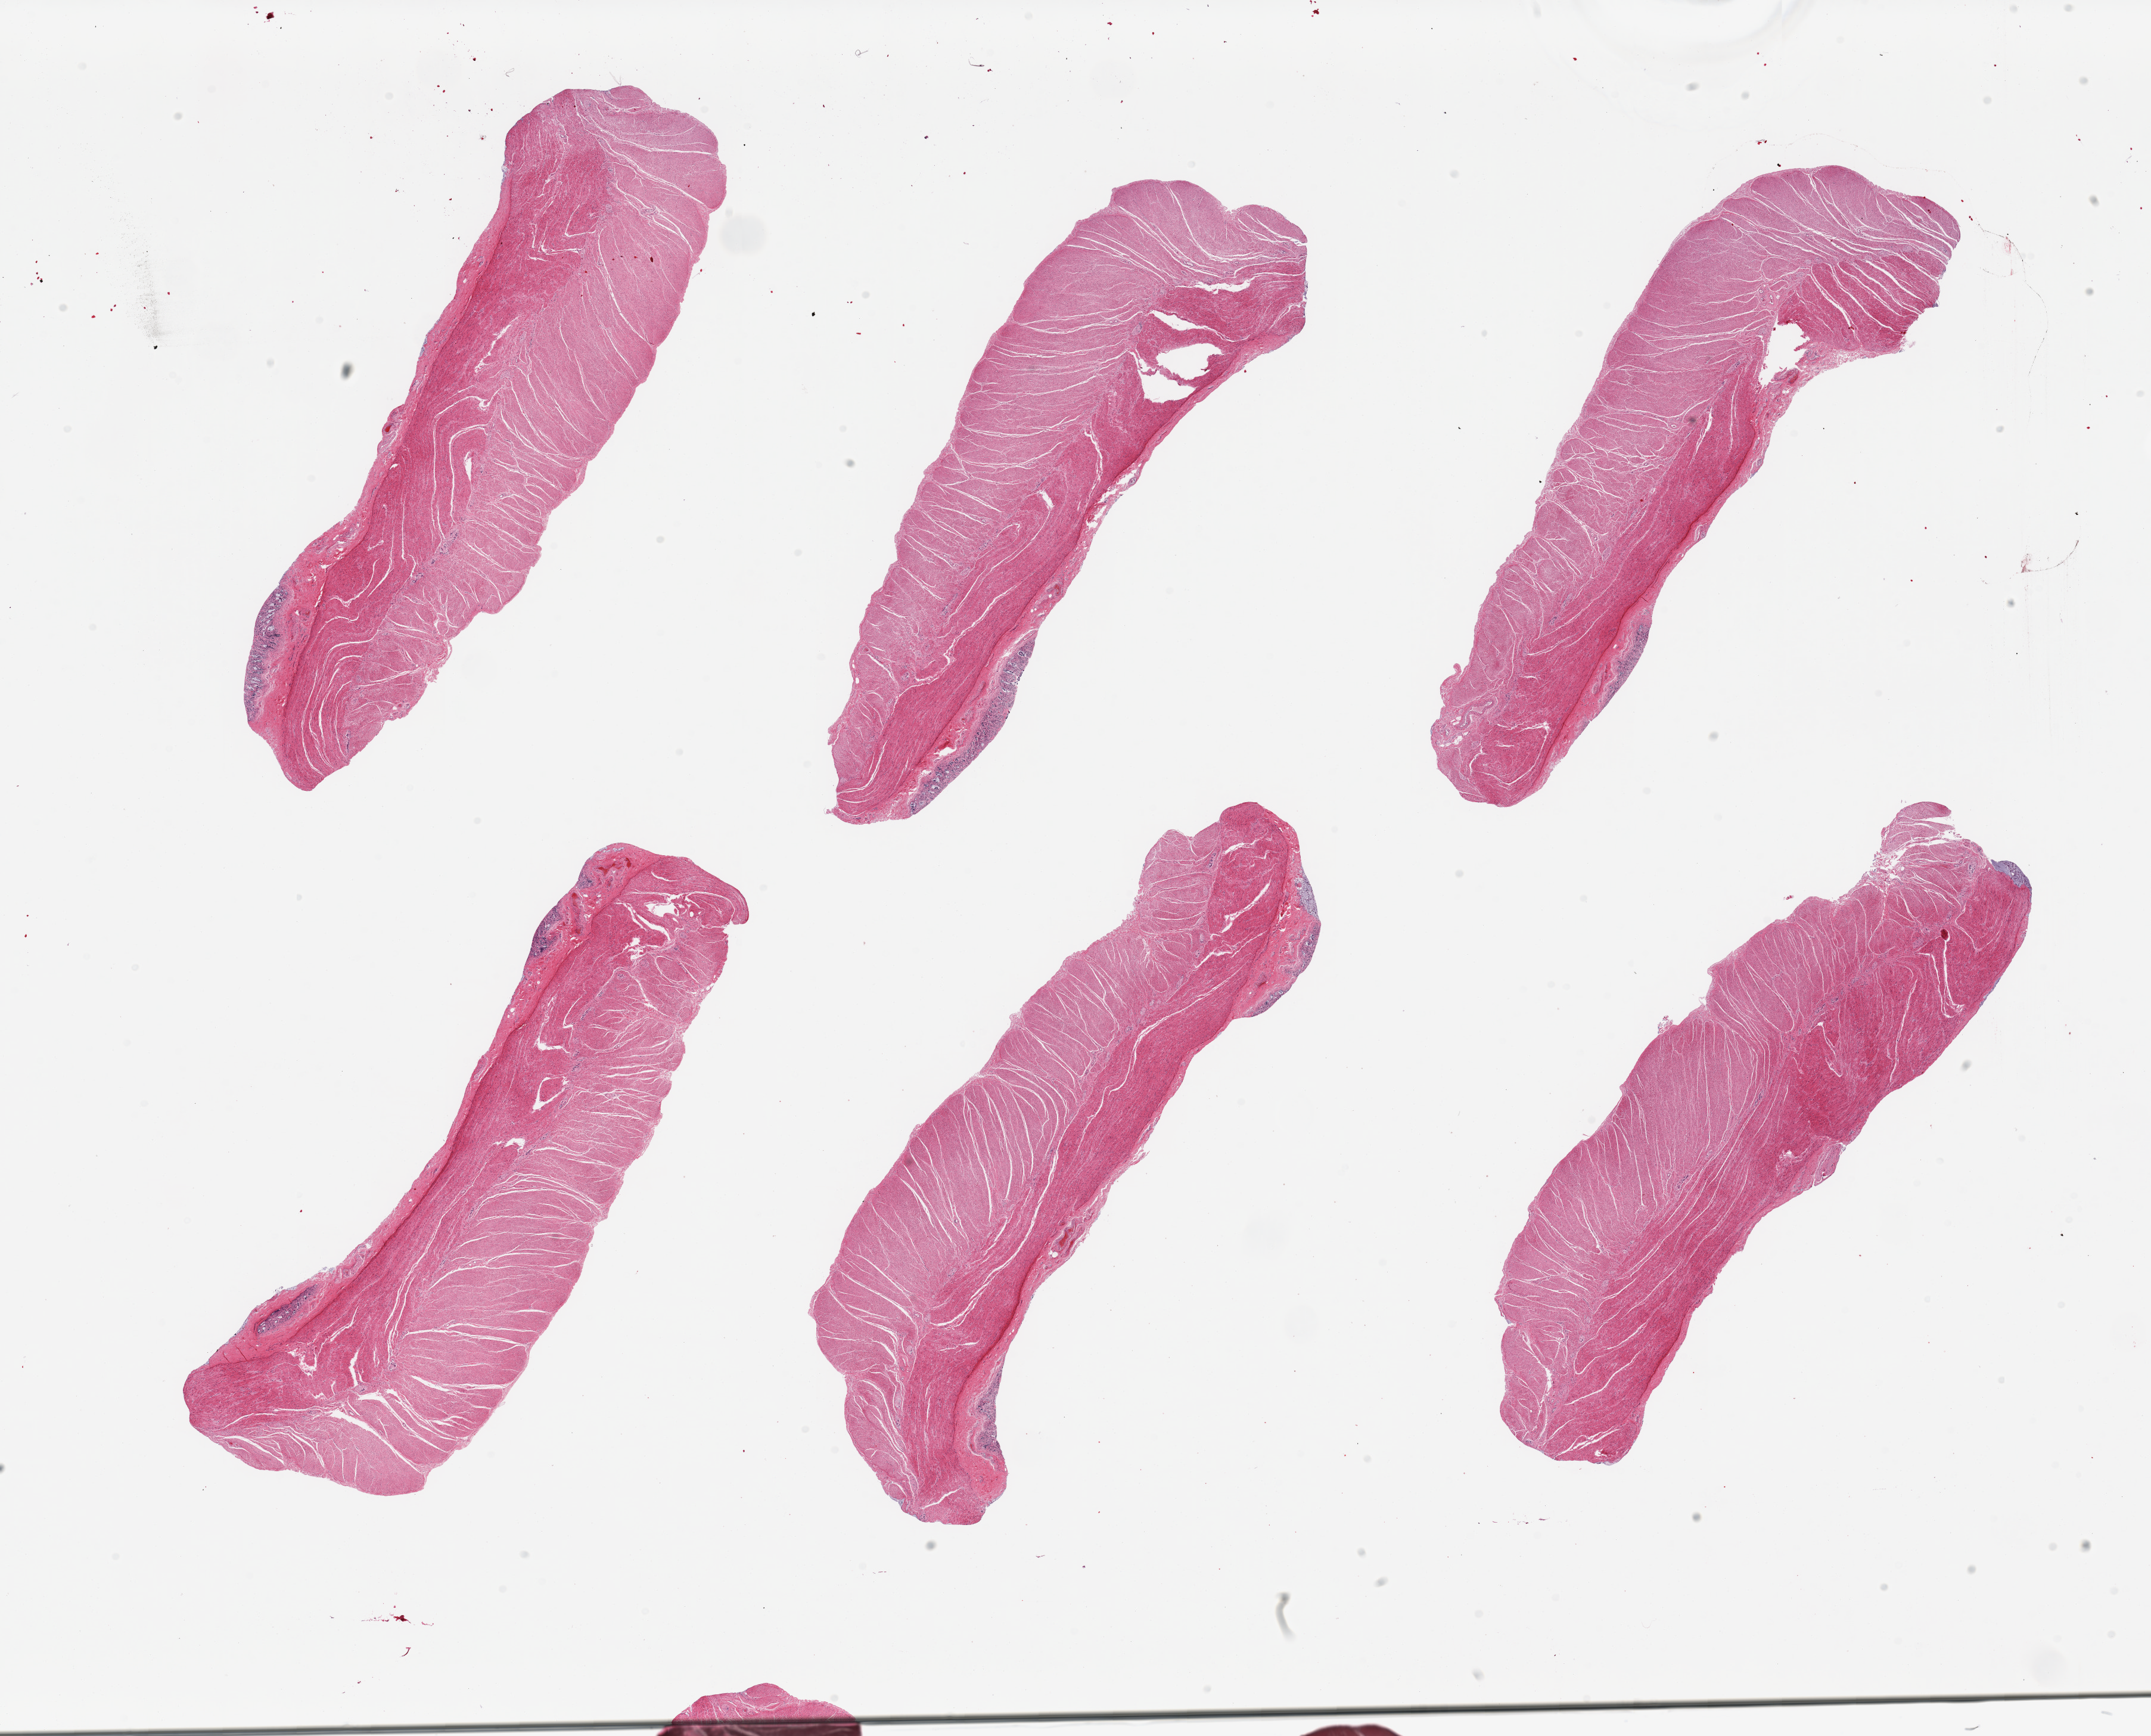
H&E whole-slide image — low-resolution overview of the scanned area, about 28.5 x 23.0 mm (from a 20x scan). PAXgene-fixed paraffin-embedded (PFPE) section. Target tissue: sigmoid colon. Donor tissue sample. Donor: male.
Pathologist's review note for this sample: 6 pieces; all have small remnants of autolyzed mucosa; muscle intact.